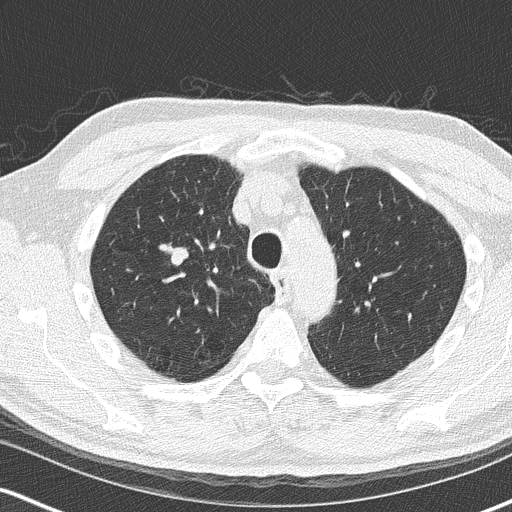
Axial slice from a low-dose chest CT screening exam; second screening round (one year after baseline); lung window (W 1500 / L -600 HU); 2 mm slice thickness; lung (sharp) reconstruction kernel (B50f); slice 53 of 170 in the series; 512 × 512 image matrix, field of view 320 × 320 mm. Male, age 68 years at enrolment.
• Lesion marked by an expert reader, bounding box [x1, y1, x2, y2] px = [152, 230, 216, 291].
• Screening reader's record for this exam (one nodule recorded; not confirmed to be the boxed lesion): non-calcified nodule or mass ≥4 mm, right upper lobe, 18 × 15 mm, smooth margins, soft tissue attenuation, pre-existing on the prior screen: no.
• Official screen result: positive, change unspecified: nodule(s) >= 4 mm or enlarging nodule(s), mass(es), or other non-specific abnormalities suspicious for lung cancer.